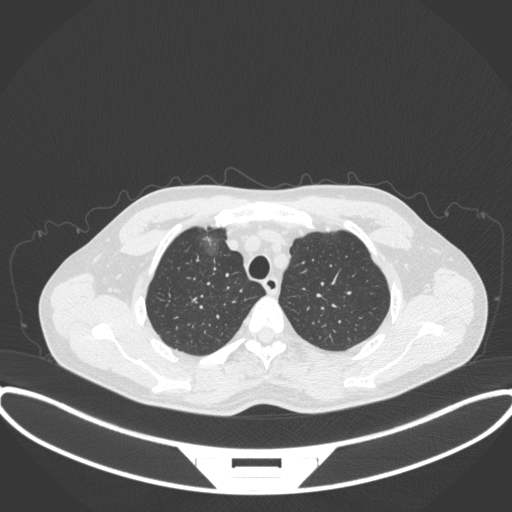
Chest CT, one axial slice; slice 300 of 395 in the series (ordered by position); 120 kVp; lung window (W 1500 / L -600 HU); 512 × 512 image matrix. Male patient, age 60 years. From the clinical record (not read from this slice): clinical TNM (as recorded): T1c N0 M0.
Outlined on this slice (rectangle marked by the reading radiologist):
- lung tumour (recorded histology: adenocarcinoma): bounding box [x1, y1, x2, y2] px = [198, 229, 223, 261]